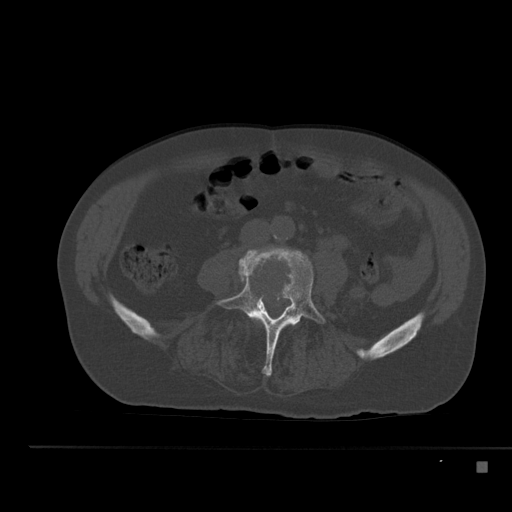
CT including the spine, one axial slice. Slice 144 of 517 in the series (ordered by position). Reconstruction kernel Br40s. Bone window (W 1800 / L 400 HU). 1.5 mm slice thickness. 512 × 512 image matrix, field of view 408 × 408 mm. Male patient, age 70 years. From the clinical record (not read from this slice): primary cancer: renal.
Outlined on this slice (semi-automatically segmented with operator editing):
- L3 vertebra: bounding box [x1, y1, x2, y2] px = [252, 318, 259, 322]
- L4 vertebra: [215, 247, 326, 377]